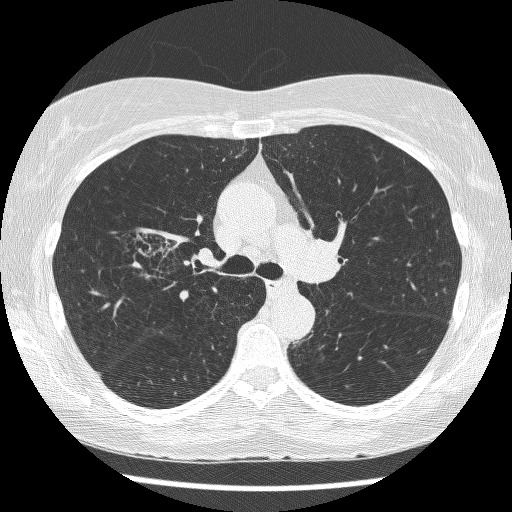
Chest CT (low-dose screening protocol), one axial image. First (baseline) screen. Lung window (W 1500 / L -600 HU). 1.25 mm slice thickness. Slice 180 of 271 in the series. Female participant, aged 64 years at enrolment. Former smoker at enrolment.
Expert-annotated lung lesion, bounding box <126,224,206,298> (left, top, right, bottom; pixels). The screening reader recorded 3 non-calcified nodules or masses ≥4 mm on this exam; which of them this box marks is not recorded. Official screen result: positive, change unspecified: nodule(s) >= 4 mm or enlarging nodule(s), mass(es), or other non-specific abnormalities suspicious for lung cancer. Lung cancer was diagnosed 735 days after this screen: adenocarcinoma, NOS, right upper lobe, right middle lobe, right hilum, stage IV (AJCC 6th edition), 85 mm at pathology.